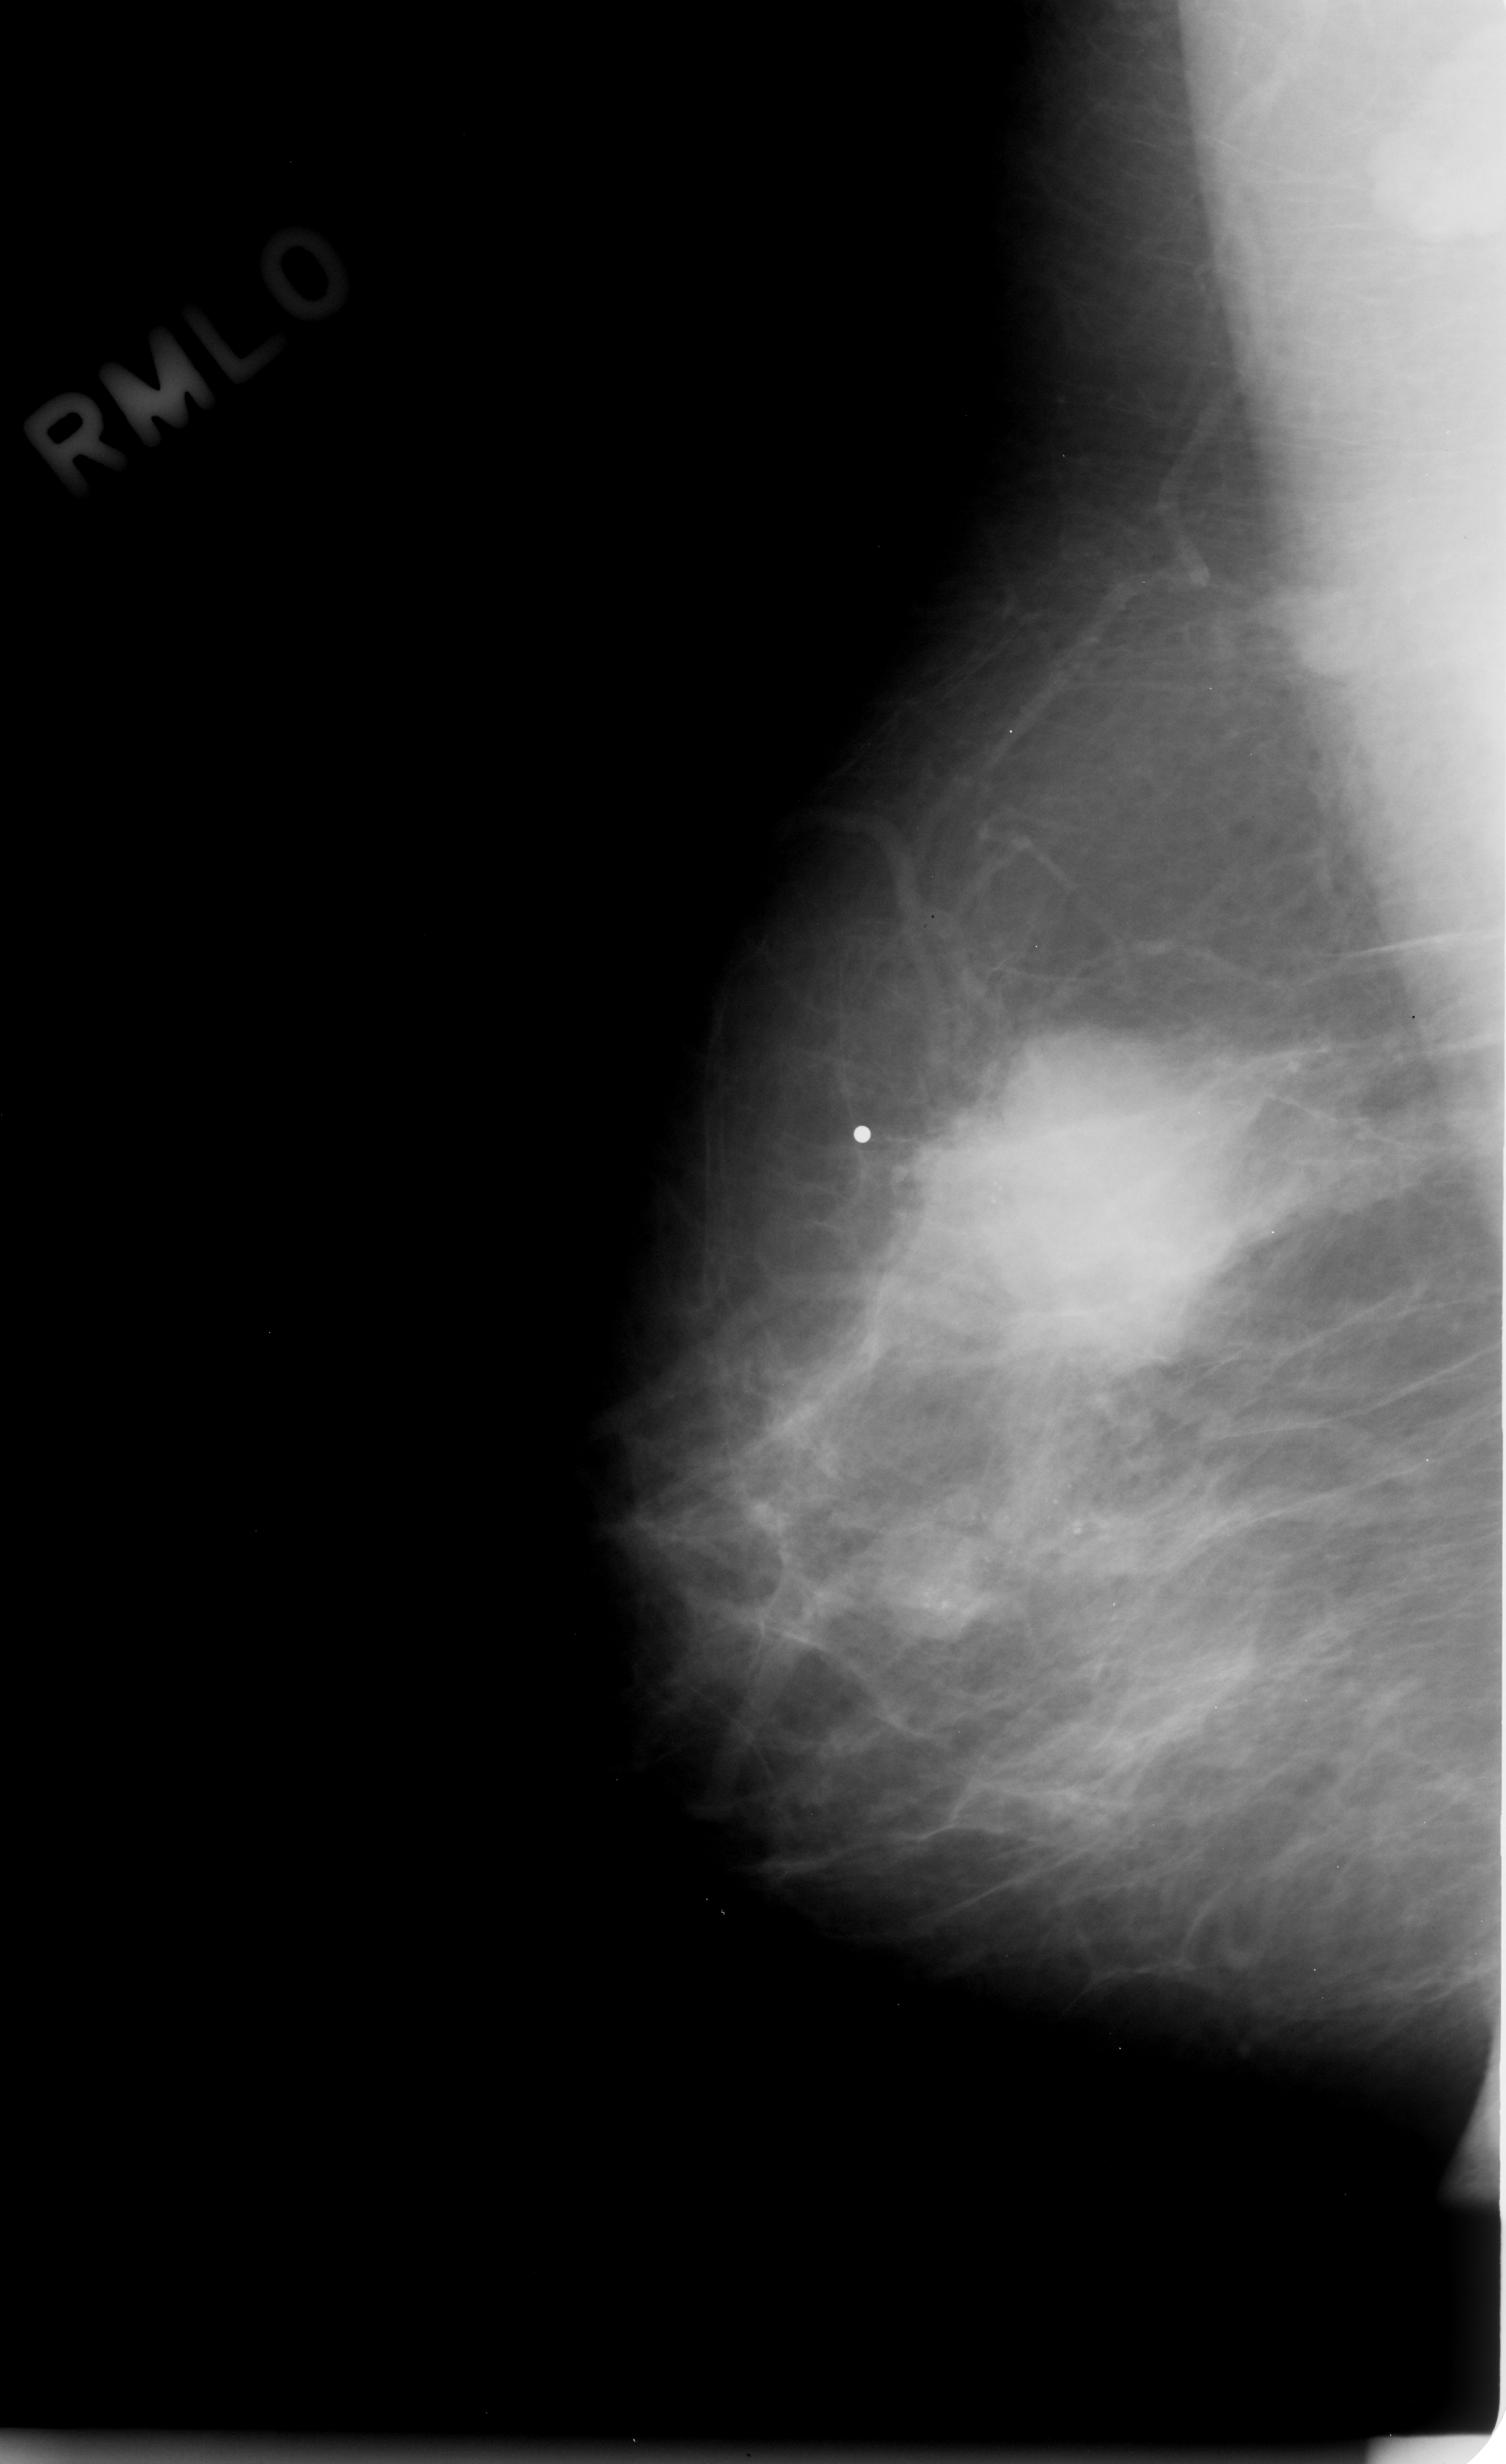
Mammogram (digitized film); right breast; mediolateral oblique (MLO) view; BI-RADS breast density category 1 (scale 1–4).
- Radiologist-marked abnormalities on this image: calcifications, morphology amorphous, distribution clustered; BI-RADS assessment category 5; pathology result (as recorded, not read from the image): malignant.